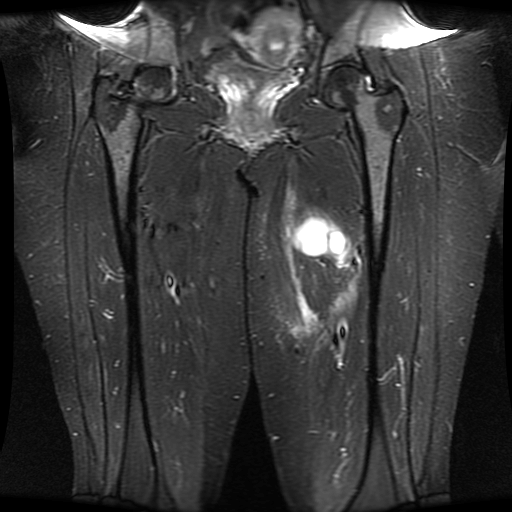
MRI of an extremity soft-tissue mass, one coronal slice. Position 15 of 30 along the scan axis. STIR. 512 × 512 image matrix. Female patient. From the clinical record (not read from this slice): histological type: myxofibrosarcoma; grade: intermediate; site of the primary tumour: left thigh.
Structures marked on this image (expert manual segmentation):
- gross tumour volume including surrounding oedema: bounding box (x1, y1, x2, y2) in pixels: (281, 190, 361, 338)
- gross tumour volume (mass): (293, 218, 347, 256)